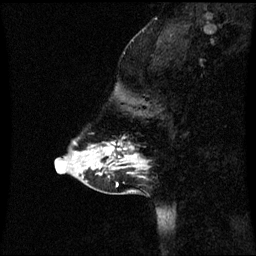
Breast MRI (dynamic contrast-enhanced), one sagittal slice; dynamic contrast-enhanced series, image 2 of 3 at this slice position (ordered by acquisition); 1.5 T; TE 4.2 ms, TR 8.9 ms; 2 mm slice thickness; 256 × 256 image matrix, field of view 220 × 220 mm. Patient: female, 43 years. Case-level facts recorded for this patient, not image findings: setting: breast cancer imaged before/during neoadjuvant chemotherapy; receptor status: HR-positive, HER2-negative.
Annotated regions visible in this slice (semi-automatic segmentation, software-assisted and operator-edited):
- analysis volume of interest (the breast-tissue region the enhancement analysis was run in; not a lesion): bounding box <84,142,144,171> (left, top, right, bottom; pixels)
- tumour enhancement mask (voxels above the 70 % enhancement threshold inside the analysis volume of interest): <103,142,136,161>